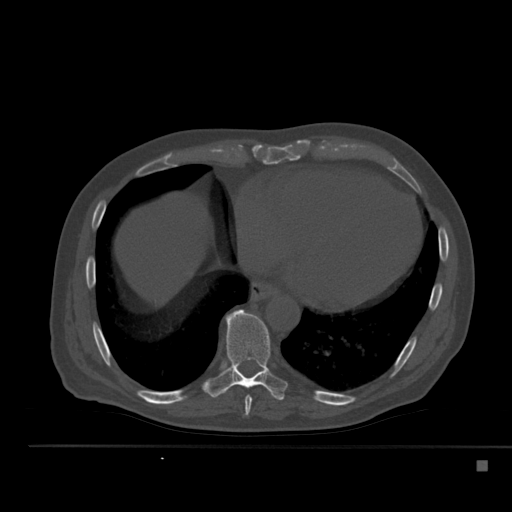
CT including the spine, one axial slice; position 291 of 517 along the scan axis; 120 kVp; bone window (W 1800 / L 400 HU); 512 × 512 image matrix, field of view 408 × 408 mm. Male patient, age 70 years. Case-level facts recorded for this patient, not image findings: primary cancer: renal.
Structures marked on this image (semi-automatically segmented with operator editing):
- T8 vertebra: bounding box (x1, y1, x2, y2) in pixels: (244, 396, 252, 416)
- T9 vertebra: (206, 309, 288, 401)